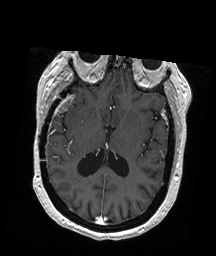
Brain MRI from a brain-tumour surgery series, one axial slice. Slice 96 of 192 in the series (ordered by position). T1-weighted post-contrast. 1 mm slice thickness. 216 × 256 image matrix. From the clinical record (not read from this slice): histopathology: Glioblastoma; WHO grade: 4; IDH mutation: no; tumour location: Right Temporal.
Outlined on this slice (outlined manually by an expert reader):
- tumour: box from (x=57, y=96) to (x=74, y=112) px